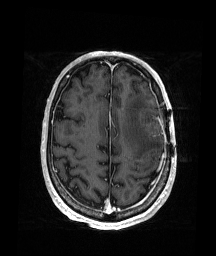
Brain MRI from a brain-tumour surgery series, one axial slice. Position 58 of 176 along the scan axis. T1-weighted post-contrast. 216 × 256 image matrix, field of view 219 × 260 mm. From the clinical record (not read from this slice): histopathology: Glioblastoma; WHO grade: 4; IDH mutation: no.
Annotated regions visible in this slice (outlined manually by an expert reader):
- tumour: bounding box [x1, y1, x2, y2] px = [143, 122, 161, 135]